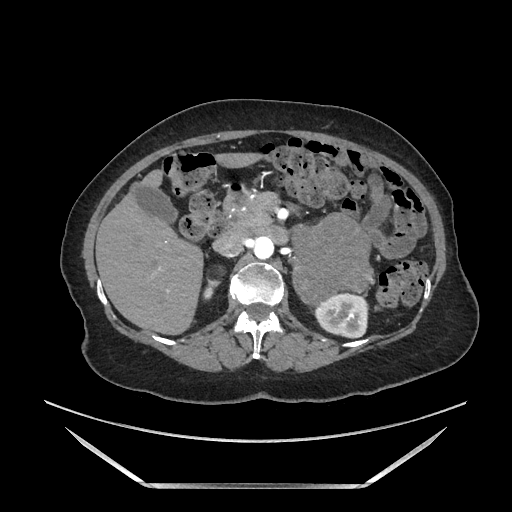
Contrast-enhanced abdominal CT, one axial slice. Position 98 of 205 along the scan axis. Soft-tissue window (W 400 / L 40 HU). 1.25 mm slice thickness. 512 × 512 image matrix, field of view 440 × 440 mm. Female patient. From the clinical record (not read from this slice): diagnosis: adrenocortical carcinoma; tumour side: left adrenal; tumour size at pathology: 12.5 cm; Ki-67 index: 39 %; stage (as recorded): 3.
Annotated regions visible in this slice (semi-automatic segmentation, software-assisted and operator-edited):
- mass: bounding box [x1, y1, x2, y2] px = [293, 218, 370, 300]